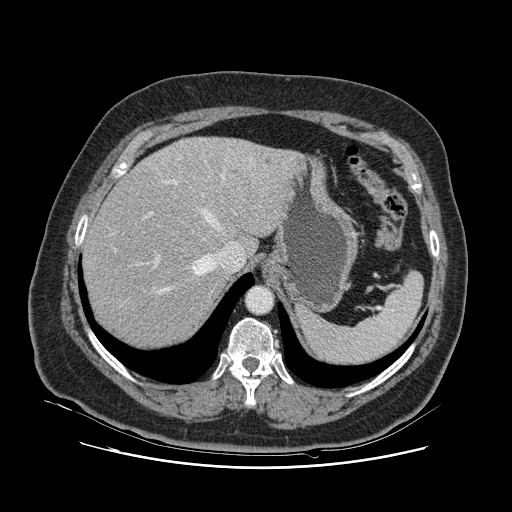
Contrast-enhanced abdominal CT, one axial slice; slice 92 of 132 in the series (ordered by position); intravenous contrast given; soft-tissue window (W 400 / L 40 HU); 2.5 mm slice thickness; 512 × 512 image matrix, field of view 391 × 391 mm. Female patient, age 73 years. From the clinical record (not read from this slice): diagnosis: colorectal cancer liver metastases, imaged before liver resection; multiple liver metastases: no; largest metastasis: 7 cm; chemotherapy before resection: yes.
Structures marked on this image (expert manual segmentation):
- hepatic veins: bounding box [x1, y1, x2, y2] px = [113, 160, 252, 293]
- liver: [84, 138, 296, 348]
- planned liver remnant (the part of the liver to remain after resection): [84, 160, 240, 348]
- portal vein (with intrahepatic branches): [115, 158, 182, 266]